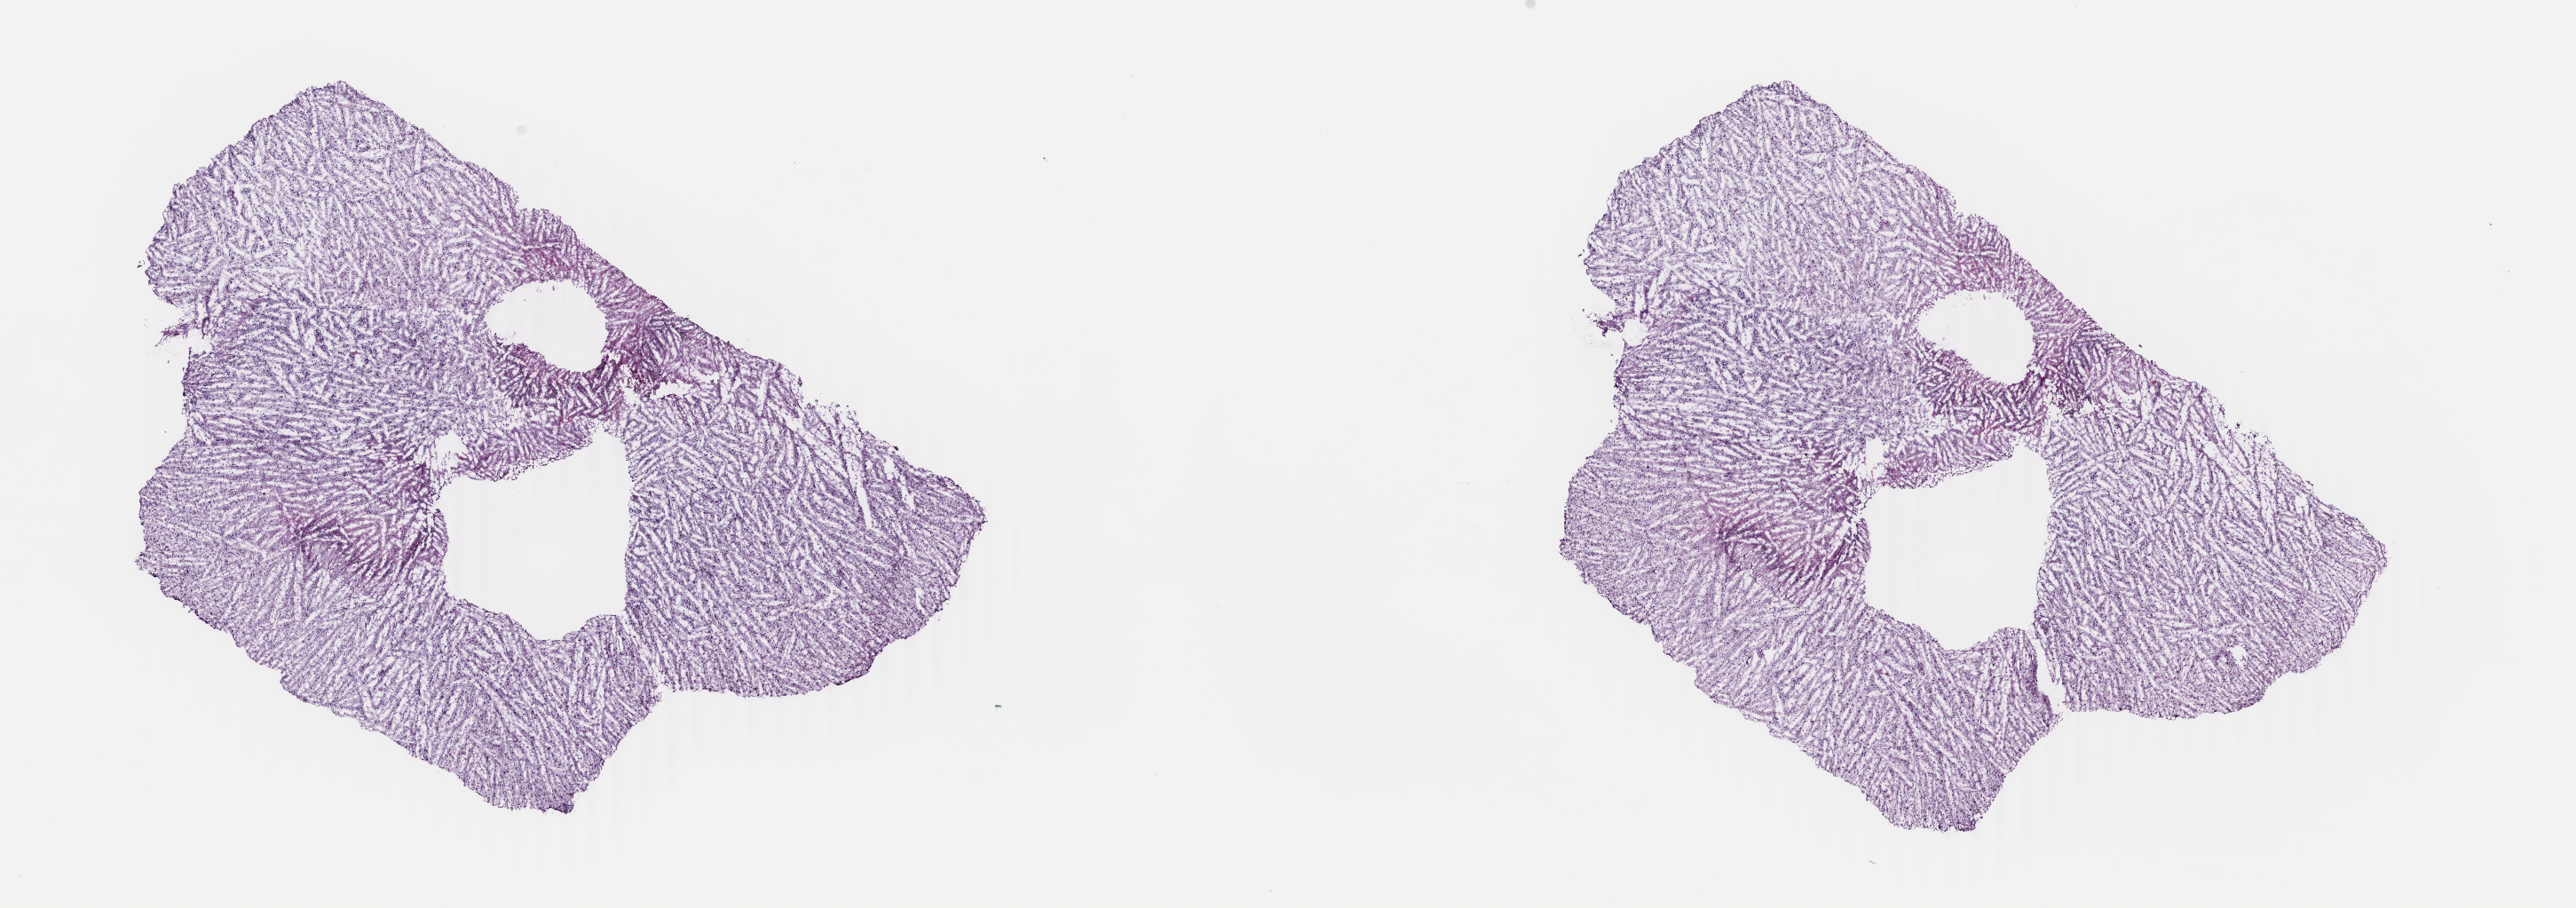
Hematoxylin and eosin (H&E) stained whole-slide image, shown as a low-resolution overview of the whole scanned area (about 23.1 x 8.1 mm, acquisition: 40x scan), frozen section from the top of the tissue portion, primary tumour sample from the brain. Patient: male, age at initial diagnosis 70 years. Histologic grade: G3 (poorly differentiated). Pathologist review of this section (percent, as recorded): tumour cells 40%, tumour nuclei 90%, normal cells 10%, stromal cells 50%, necrosis 0%. Infiltration values recorded for this section: lymphocyte infiltration 0%, monocyte infiltration 0%, neutrophil infiltration 0%.
• diagnosis: Astrocytoma, anaplastic (cerebrum)